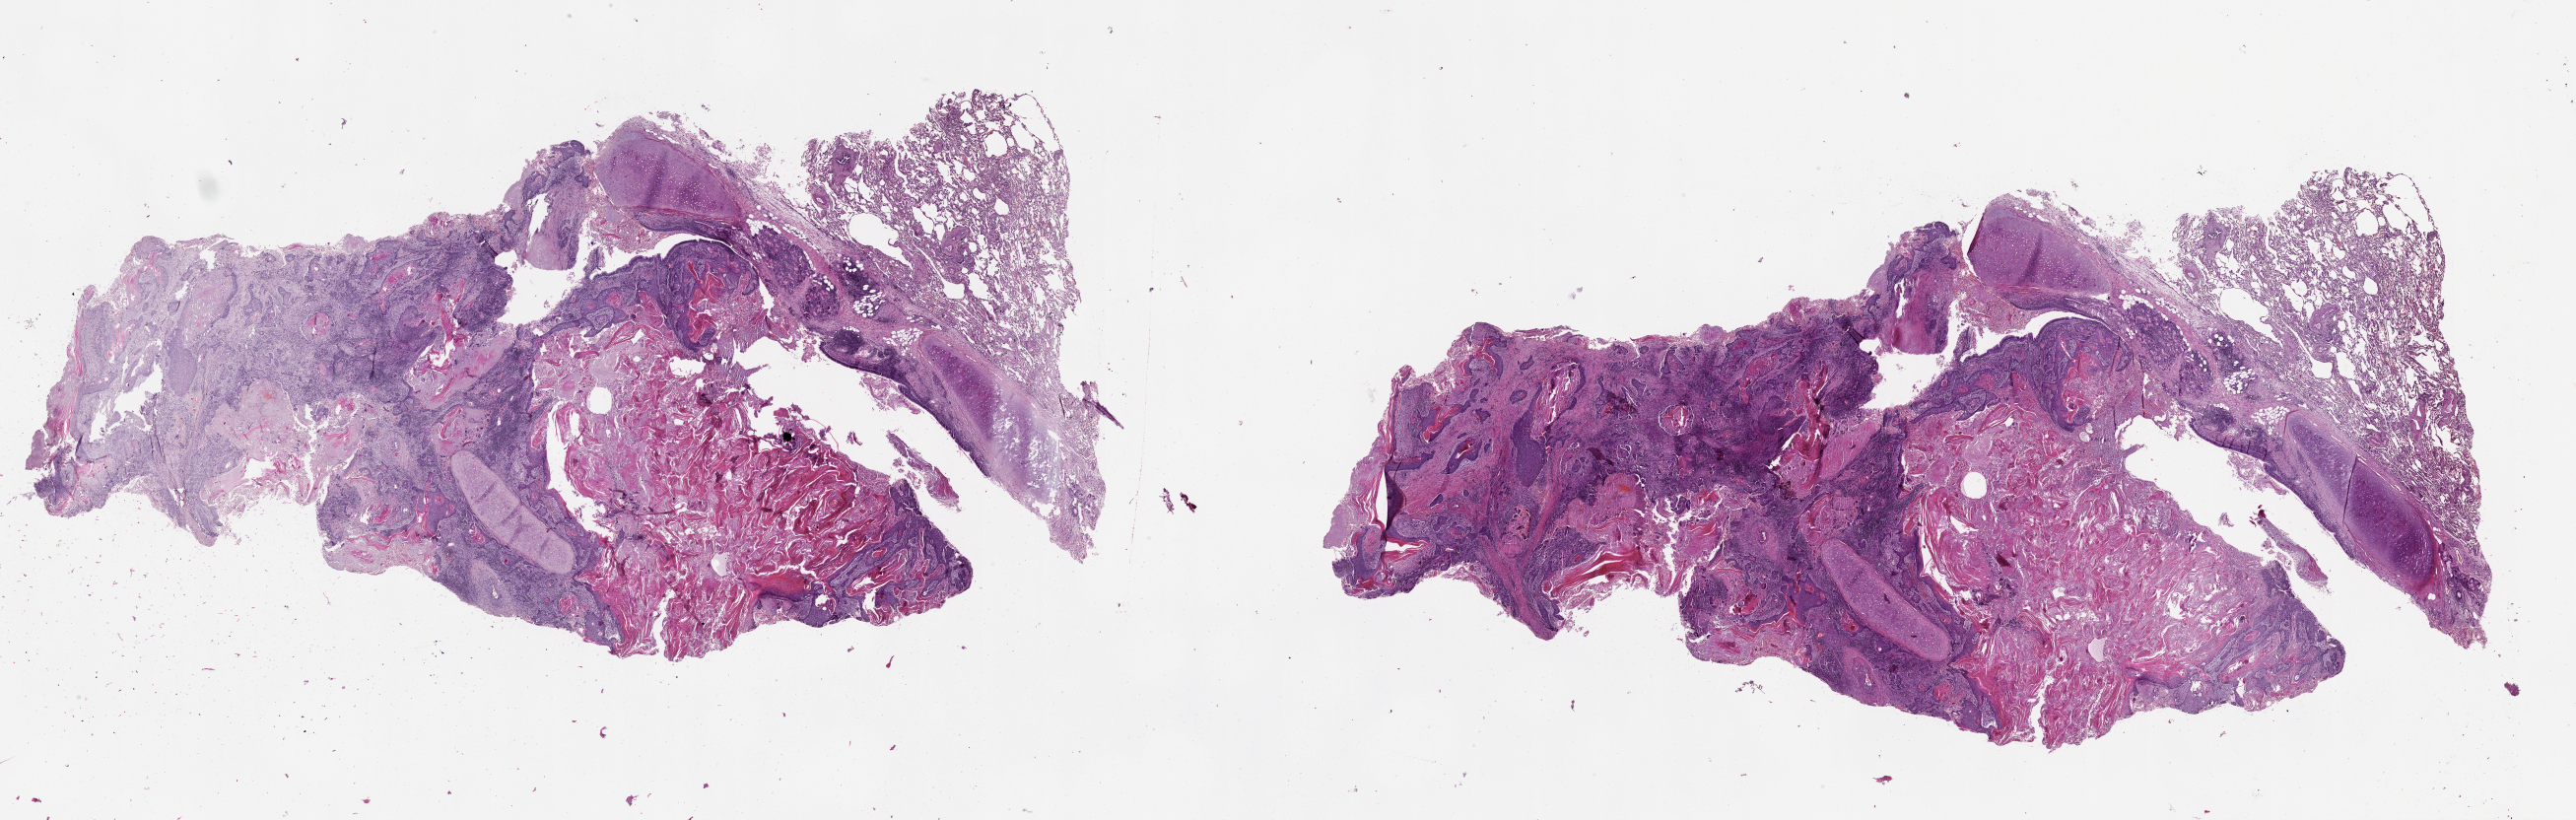
Hematoxylin and eosin (H&E) stained whole-slide image — shown as a low-resolution overview of the whole scanned area (about 42.1 x 13.4 mm, slide scanned at 20x). Lung, tumour tissue. Male, 72 y/o.
Patient diagnosis (cohort enrolment): squamous cell carcinoma (lung).